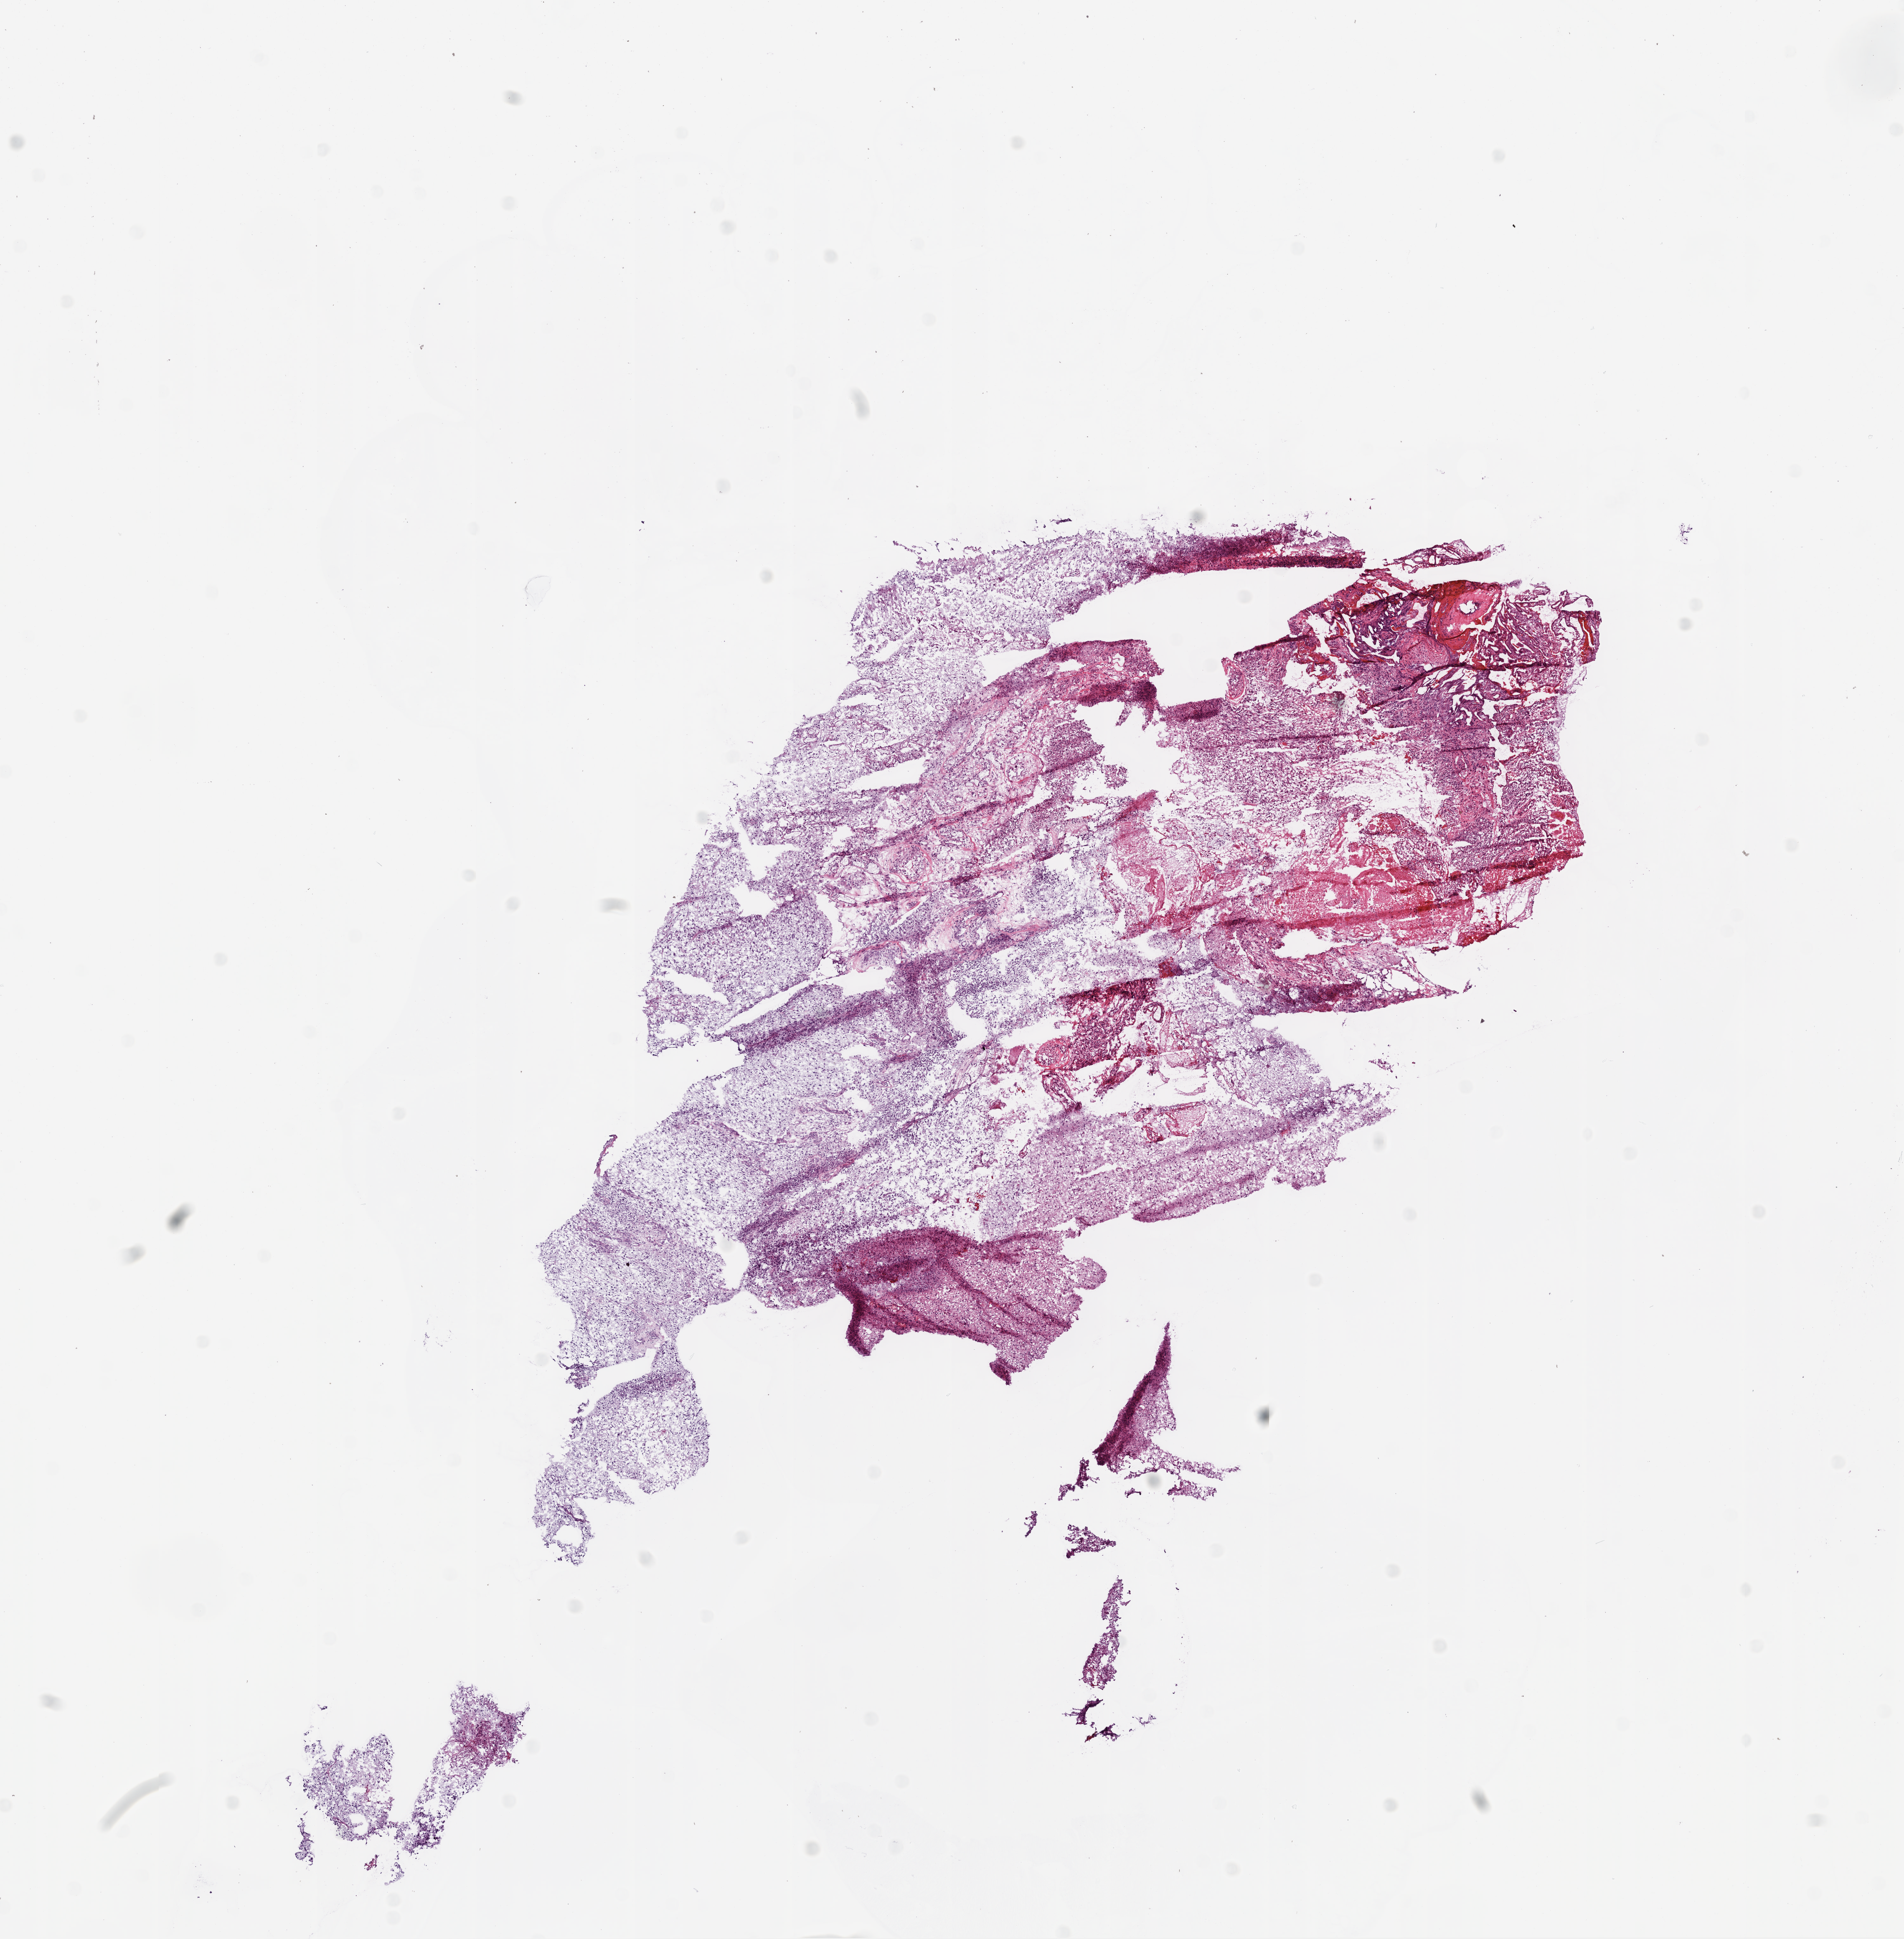
Whole-slide histology image, H&E-stained — low-resolution overview of the scanned area, about 12.0 x 12.3 mm (from a 20x scan), frozen section from the bottom of the tissue portion, brain, primary tumour sample. Male, age 67 years at initial diagnosis. Slide review estimates, as recorded: tumour cells 60%, tumour nuclei 85%.
Pathologic diagnosis: Glioblastoma.